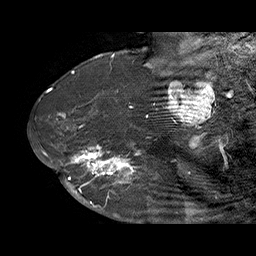
Breast MRI (dynamic contrast-enhanced), one sagittal slice. Position 46 of 70 along the scan axis. Dynamic contrast-enhanced series, time point 2 of 6 at this slice position (early post-contrast). 1.5 T. TE 4.5 ms, TR 32.4 ms. 3 mm slice thickness. 256 × 256 image matrix, field of view 180 × 180 mm. Female patient. Case-level facts recorded for this patient, not image findings: setting: breast cancer imaged before/during neoadjuvant chemotherapy; receptor status: HR-positive, HER2-negative.
Structures marked on this image (semi-automatic segmentation, software-assisted and operator-edited):
- analysis volume of interest (the breast-tissue region the enhancement analysis was run in; not a lesion): box from (x=71, y=128) to (x=159, y=202) px
- tumour enhancement mask (voxels above the 100 % enhancement threshold inside the analysis volume of interest): (x=71, y=128)–(x=143, y=202)